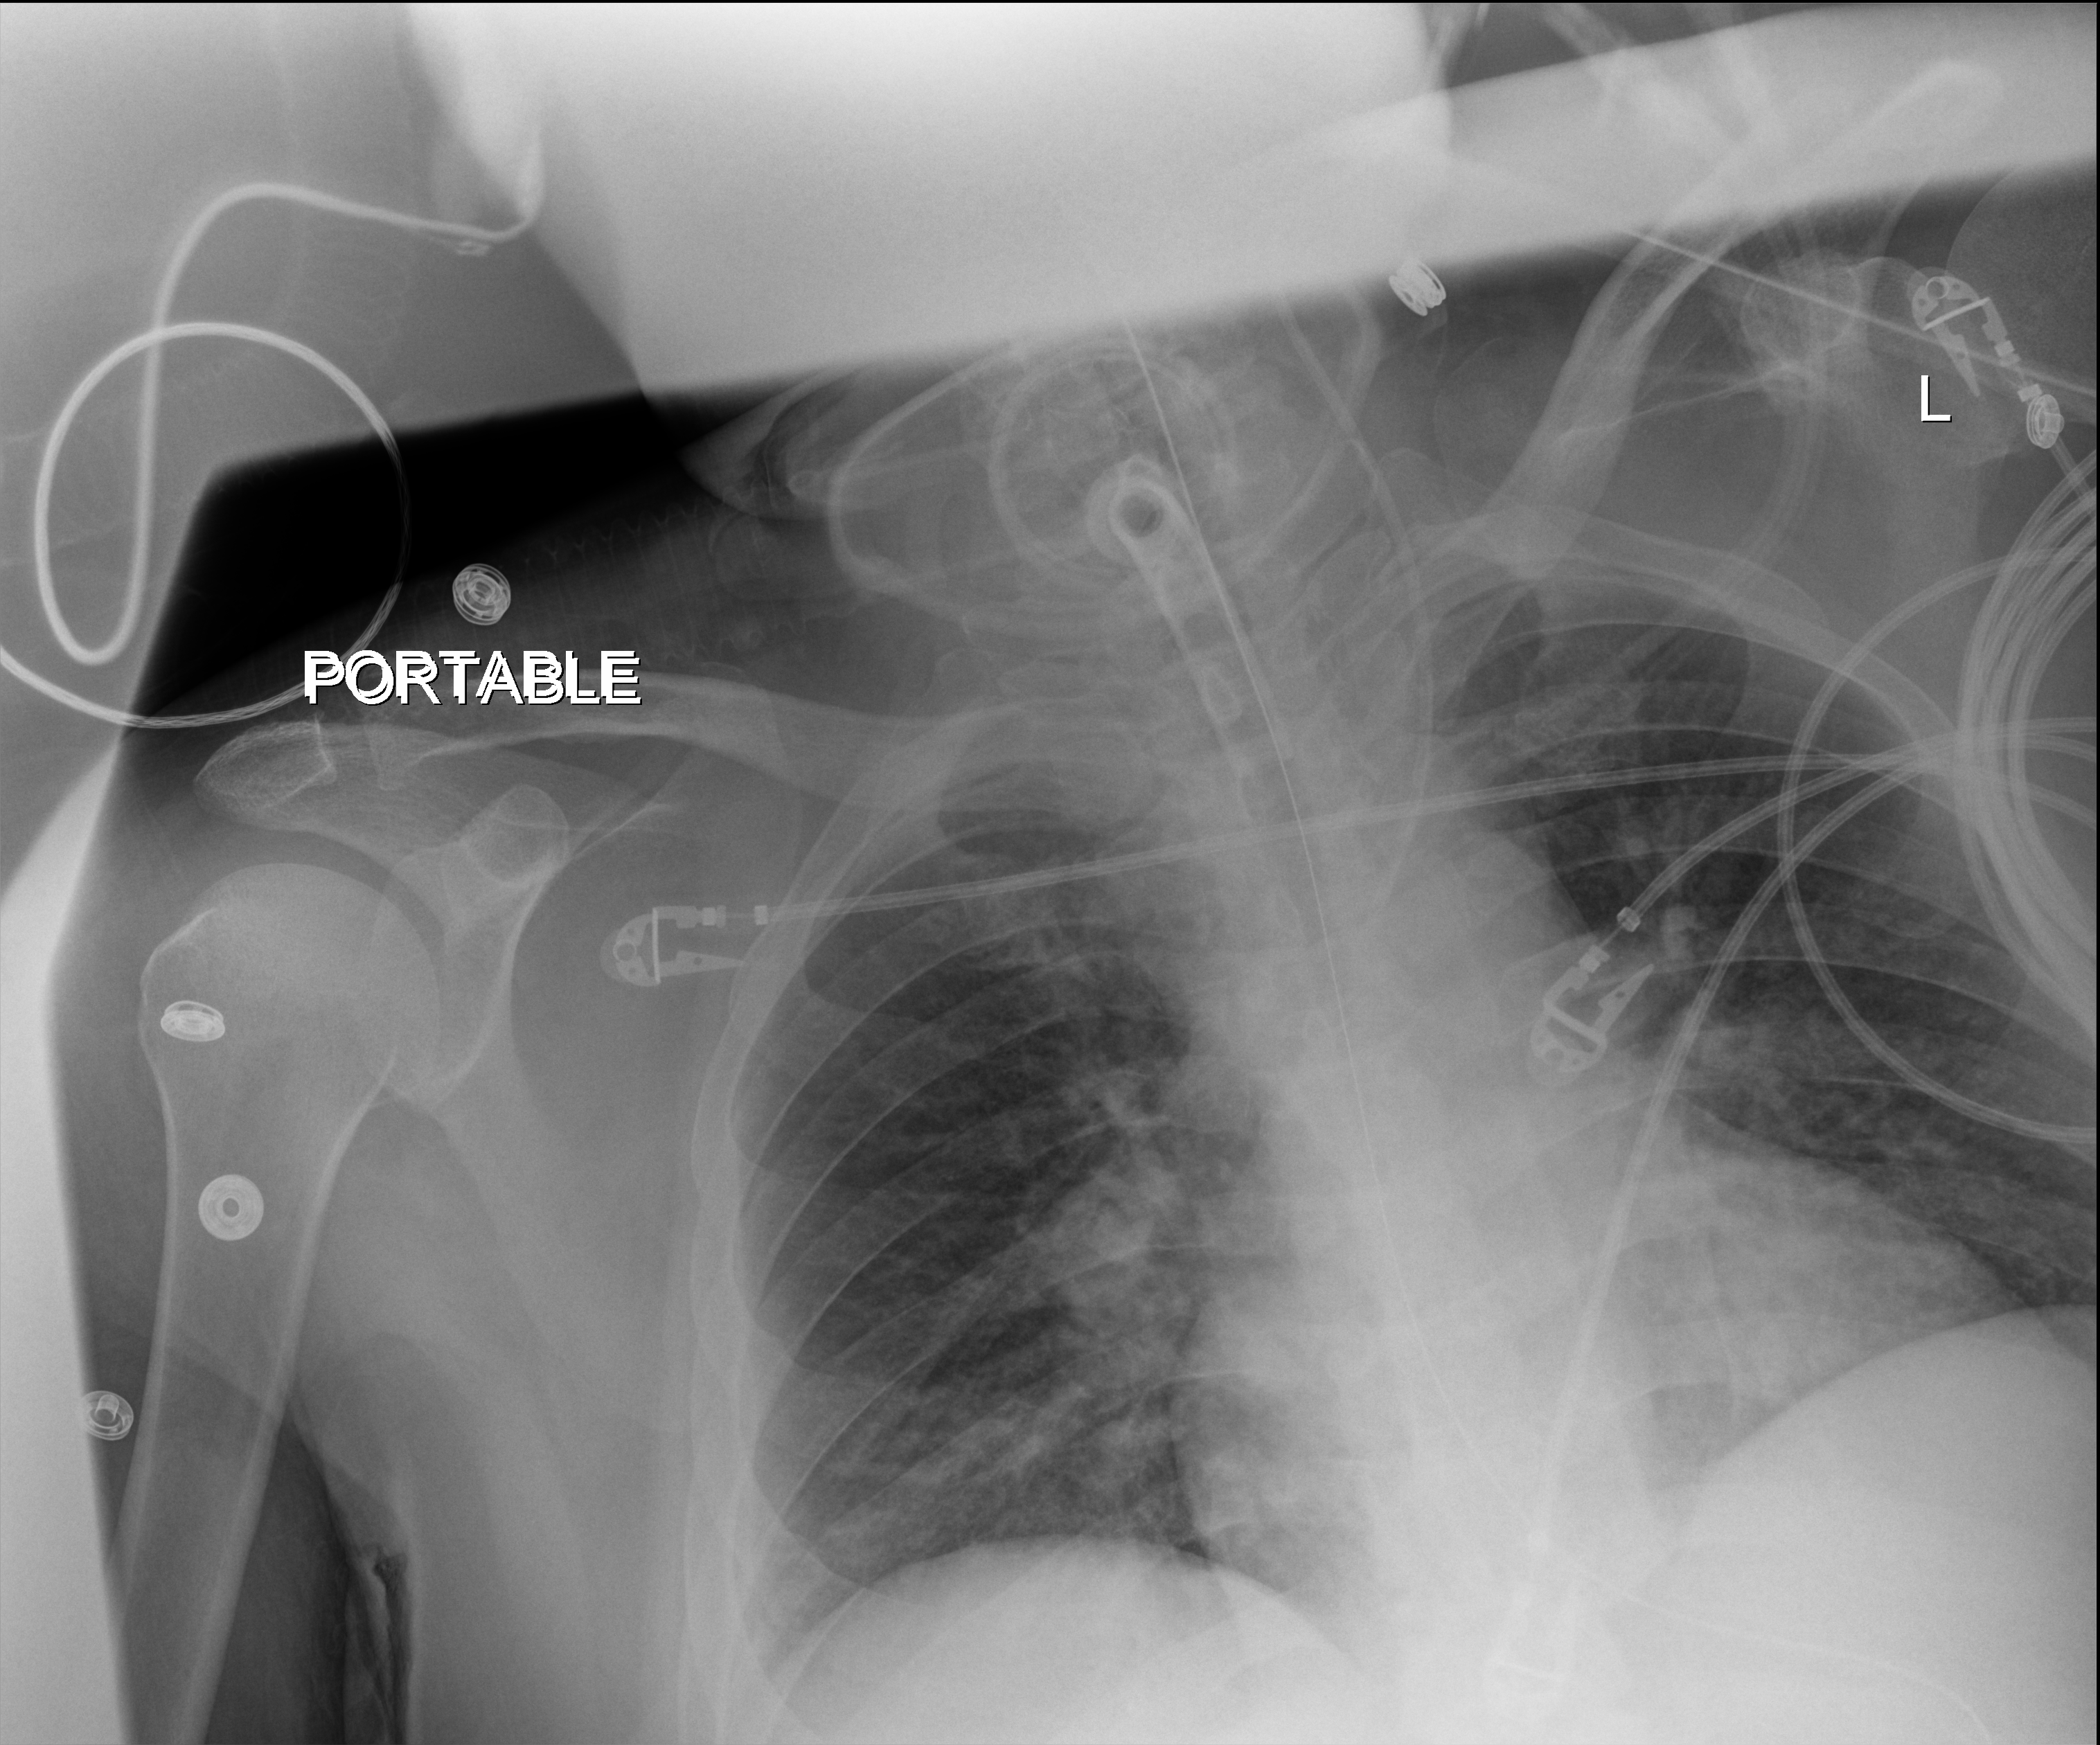
Chest X-ray (portable), anteroposterior (AP) projection. Patient hospitalised with COVID-19; female, aged 75–90 years.
Hospital-stay facts (about this admission, not read from this image; timing relative to this image not recorded):
- length of hospital stay: 70 days
- admitted to intensive care during this hospital stay: yes
- mechanically ventilated during this hospital stay: yes